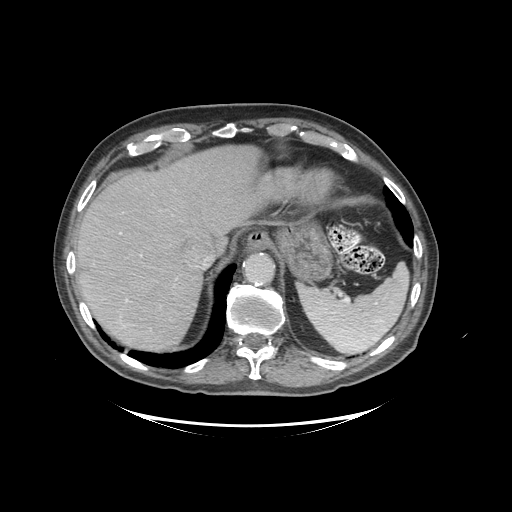
Contrast-enhanced abdominal CT (liver protocol), one axial slice. Position 78 of 99 along the scan axis. Soft-tissue window (W 400 / L 40 HU). 2.5 mm slice thickness. 512 × 512 image matrix, field of view 460 × 460 mm. From the clinical record (not read from this slice): diagnosis: hepatocellular carcinoma (patient treated with transarterial chemoembolisation; whether this scan precedes or follows treatment is not stated here); TNM stage (as recorded): Stage-I; Child-Pugh class: A; tumour differentiation: moderately differentiated; tumour nodularity: uninodular.
Annotated regions visible in this slice (semi-automatically segmented with operator editing):
- liver parenchyma outside the tumour (the mass and vessels are separate outlines, so this box may not span the whole liver): box from (x=76, y=146) to (x=298, y=350) px
- liver vessels: (x=120, y=232)–(x=207, y=328)